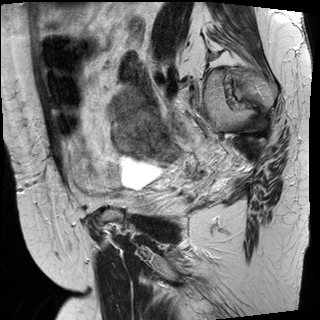
Pelvic MRI for cervical cancer, one sagittal slice; slice 23 of 30 in the series (ordered by position); T2-weighted; 1.5 T; TE 89 ms, TR 3810 ms; 320 × 320 image matrix. Female patient, age 62 years.
Structures marked on this image (manually delineated by an expert):
- uterus and cervix: box from (x=112, y=109) to (x=180, y=164) px